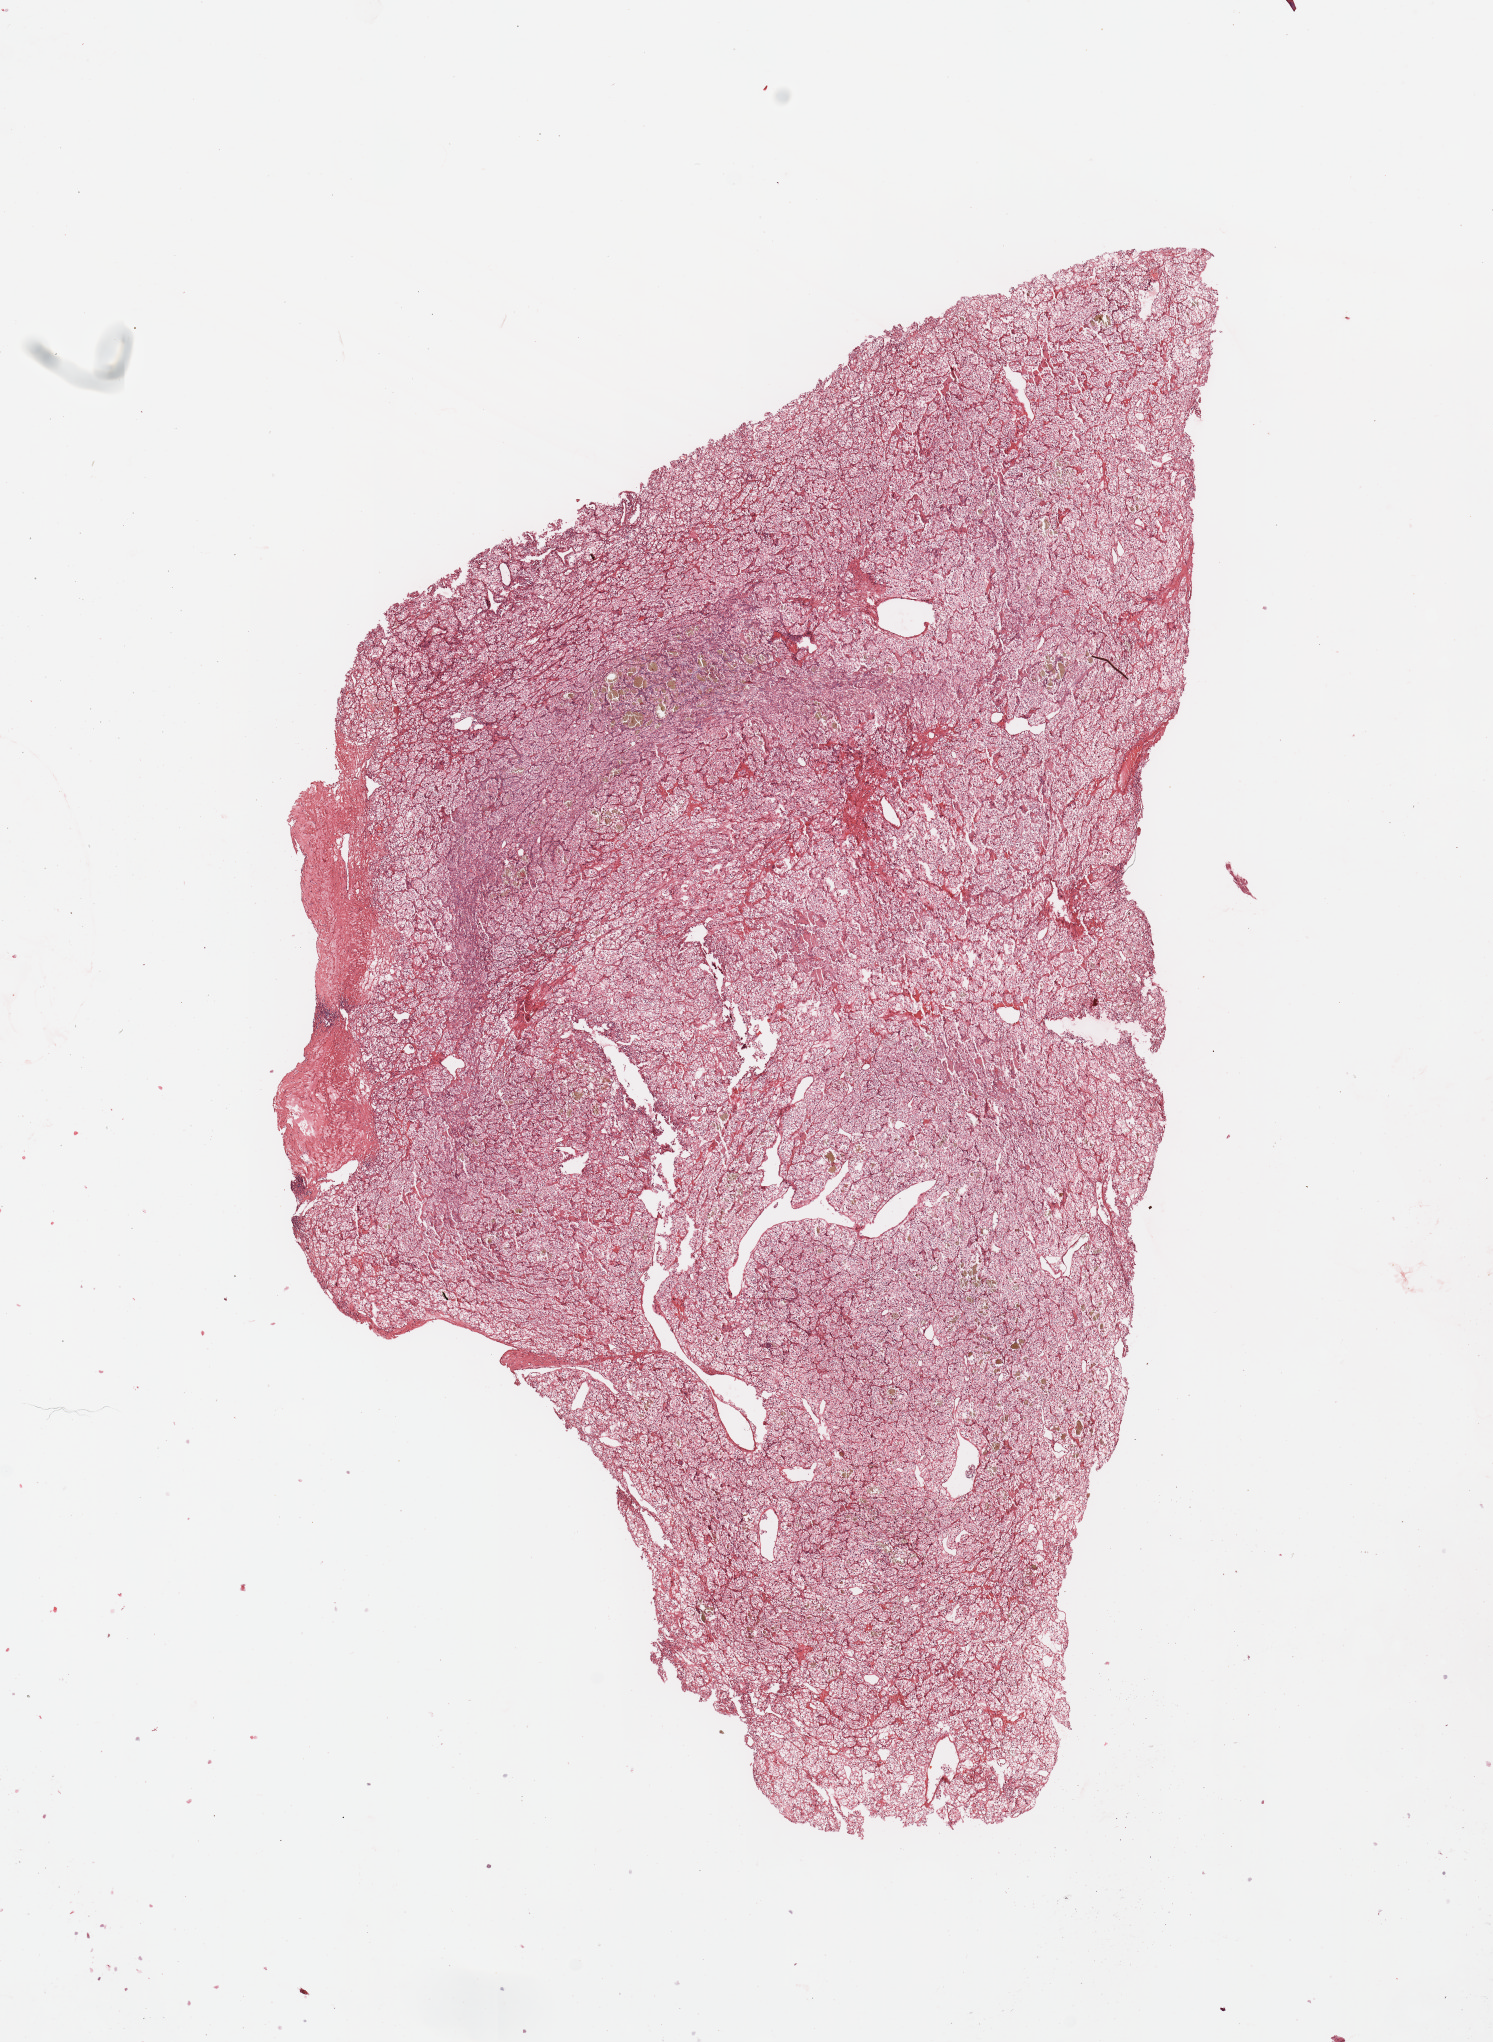
Digitized H&E-stained tissue section (whole slide), low-resolution overview of the scanned area, about 11.8 x 16.2 mm (from a 20x scan); tumour tissue sample, sampled site: kidney. Patient: male, age 65 years. Histologic grade: G2 (moderately differentiated). Slide review estimates, as recorded: tumour nuclei 90%, necrosis 5%.
Primary tumour site (as recorded): upper pole. Diagnosis: Renal cell carcinoma, NOS. AJCC pathologic stage: III.